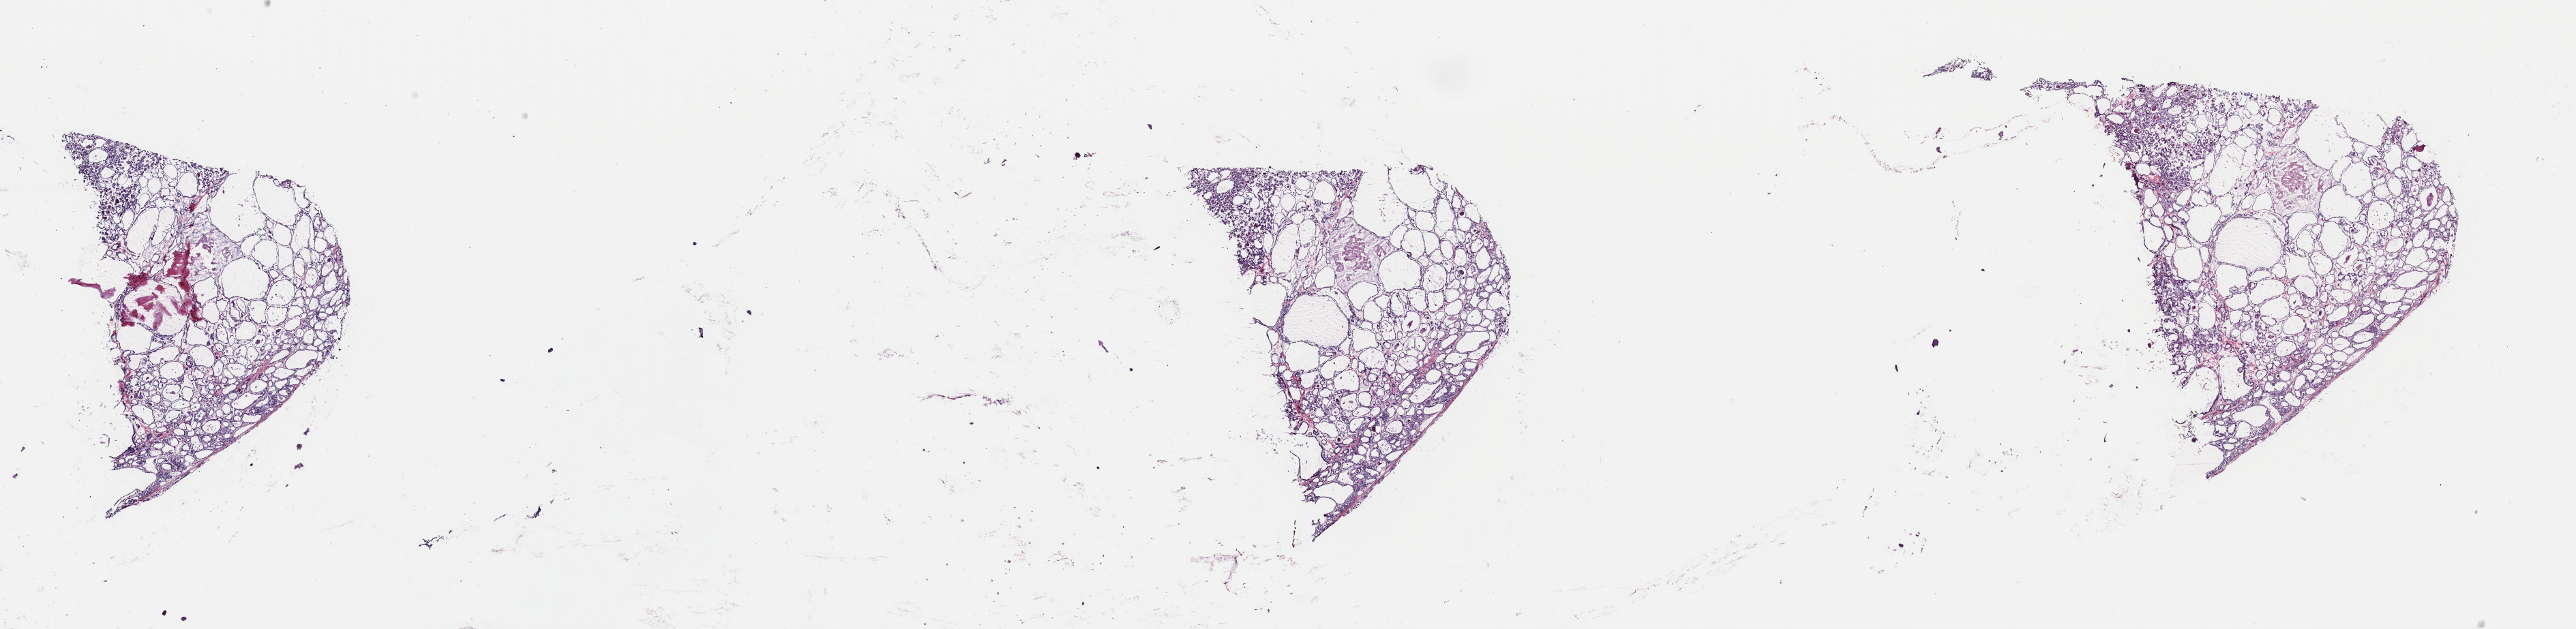
H&E whole-slide image, whole scanned area (about 29.8 x 7.3 mm, slide scanned at 40x) shown as a low-resolution overview, frozen section from the top of the tissue portion, thyroid, primary tumour sample. Patient: female, age at initial diagnosis 48 years.
Pathologic diagnosis: Papillary carcinoma, follicular variant (thyroid gland).